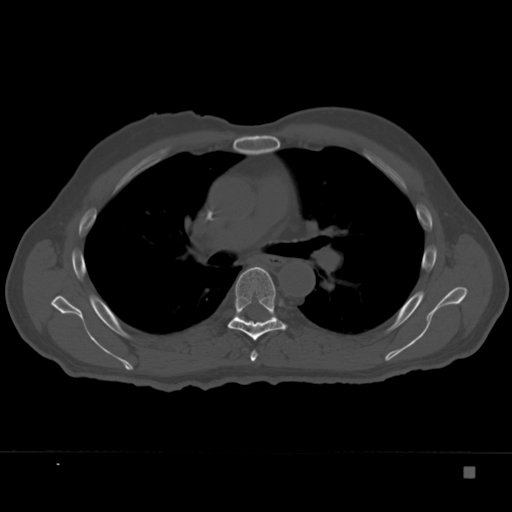
CT including the spine, one axial slice. Position 241 of 332 along the scan axis. Reconstruction kernel Br40s. 120 kVp. Bone window (W 1800 / L 400 HU). 1.5 mm slice thickness. 512 × 512 image matrix, field of view 389 × 389 mm. Male patient, age 72 years. From the clinical record (not read from this slice): primary cancer: skeletal.
Annotated regions visible in this slice (semi-automatic segmentation, software-assisted and operator-edited):
- T5 vertebra: bounding box <250,351,258,362> (left, top, right, bottom; pixels)
- T6 vertebra: <228,267,286,341>